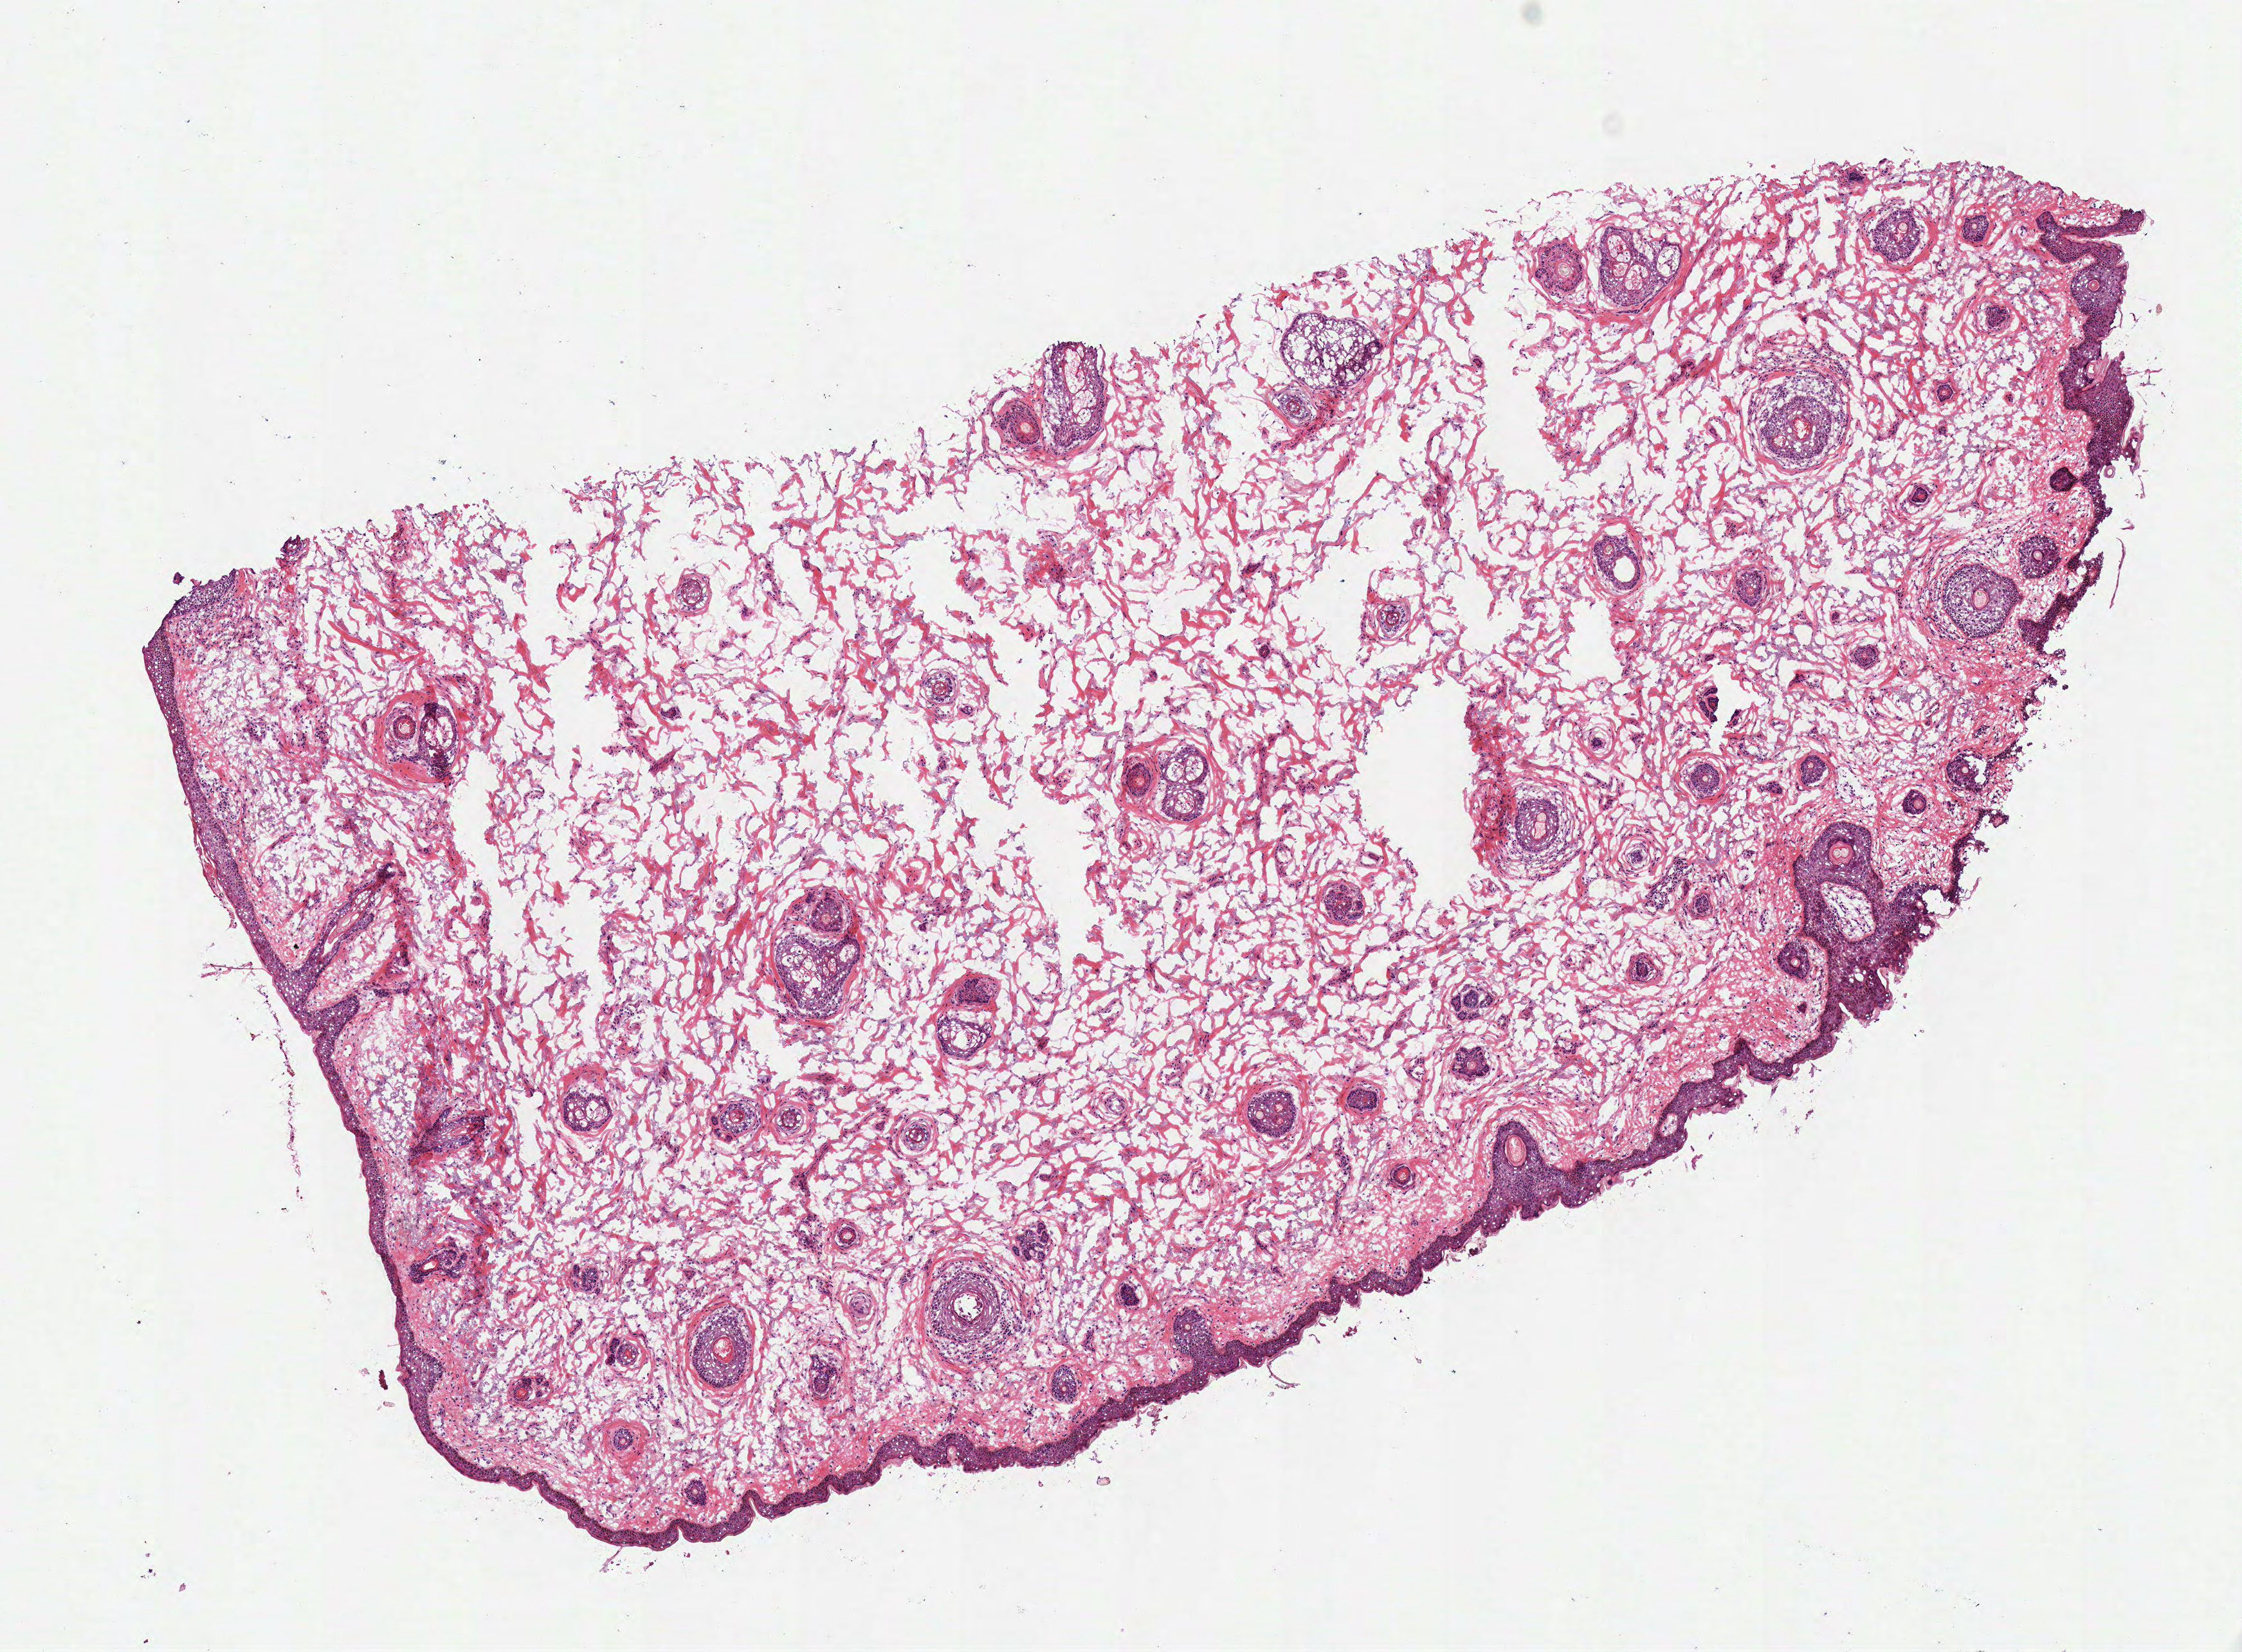
Whole-slide histology image, H&E-stained — low-resolution overview of the scanned area, about 6.9 x 5.0 mm, frozen section, sample: solid tissue normal (non-tumour tissue), head and neck. Female, age 87 years at initial diagnosis.
- this section: solid tissue normal (non-tumour) sample from the same patient
- patient diagnosis: Squamous cell carcinoma, NOS (overlapping lesion of lip, oral cavity and pharynx)